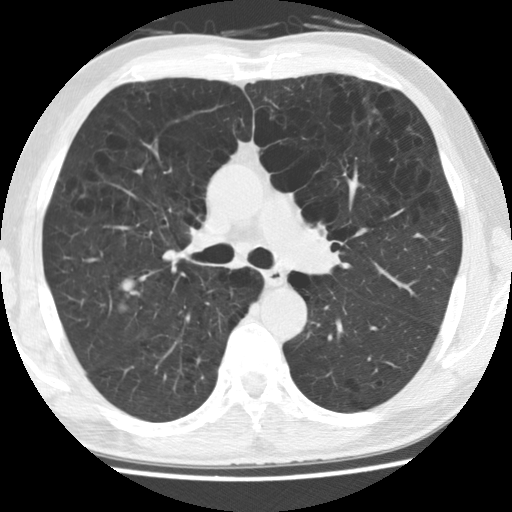
Chest CT (low-dose screening protocol), one axial image; baseline annual screen; lung window (W 1500 / L -600 HU); standard (soft-tissue) reconstruction kernel (STANDARD). Male, age 62 years at enrolment.
Expert-annotated lung lesion, bounding box [x1, y1, x2, y2] px = [95, 261, 151, 324]. The screening reader recorded 2 non-calcified nodules or masses ≥4 mm on this exam; which of them this box marks is not recorded. Official screen result: positive, change unspecified: nodule(s) >= 4 mm or enlarging nodule(s), mass(es), or other non-specific abnormalities suspicious for lung cancer. Later outcome: lung cancer diagnosed 288 days after this screen — oat cell carcinoma, right upper lobe, undifferentiated (G4), stage IV (AJCC 6th edition), 30 mm at pathology.